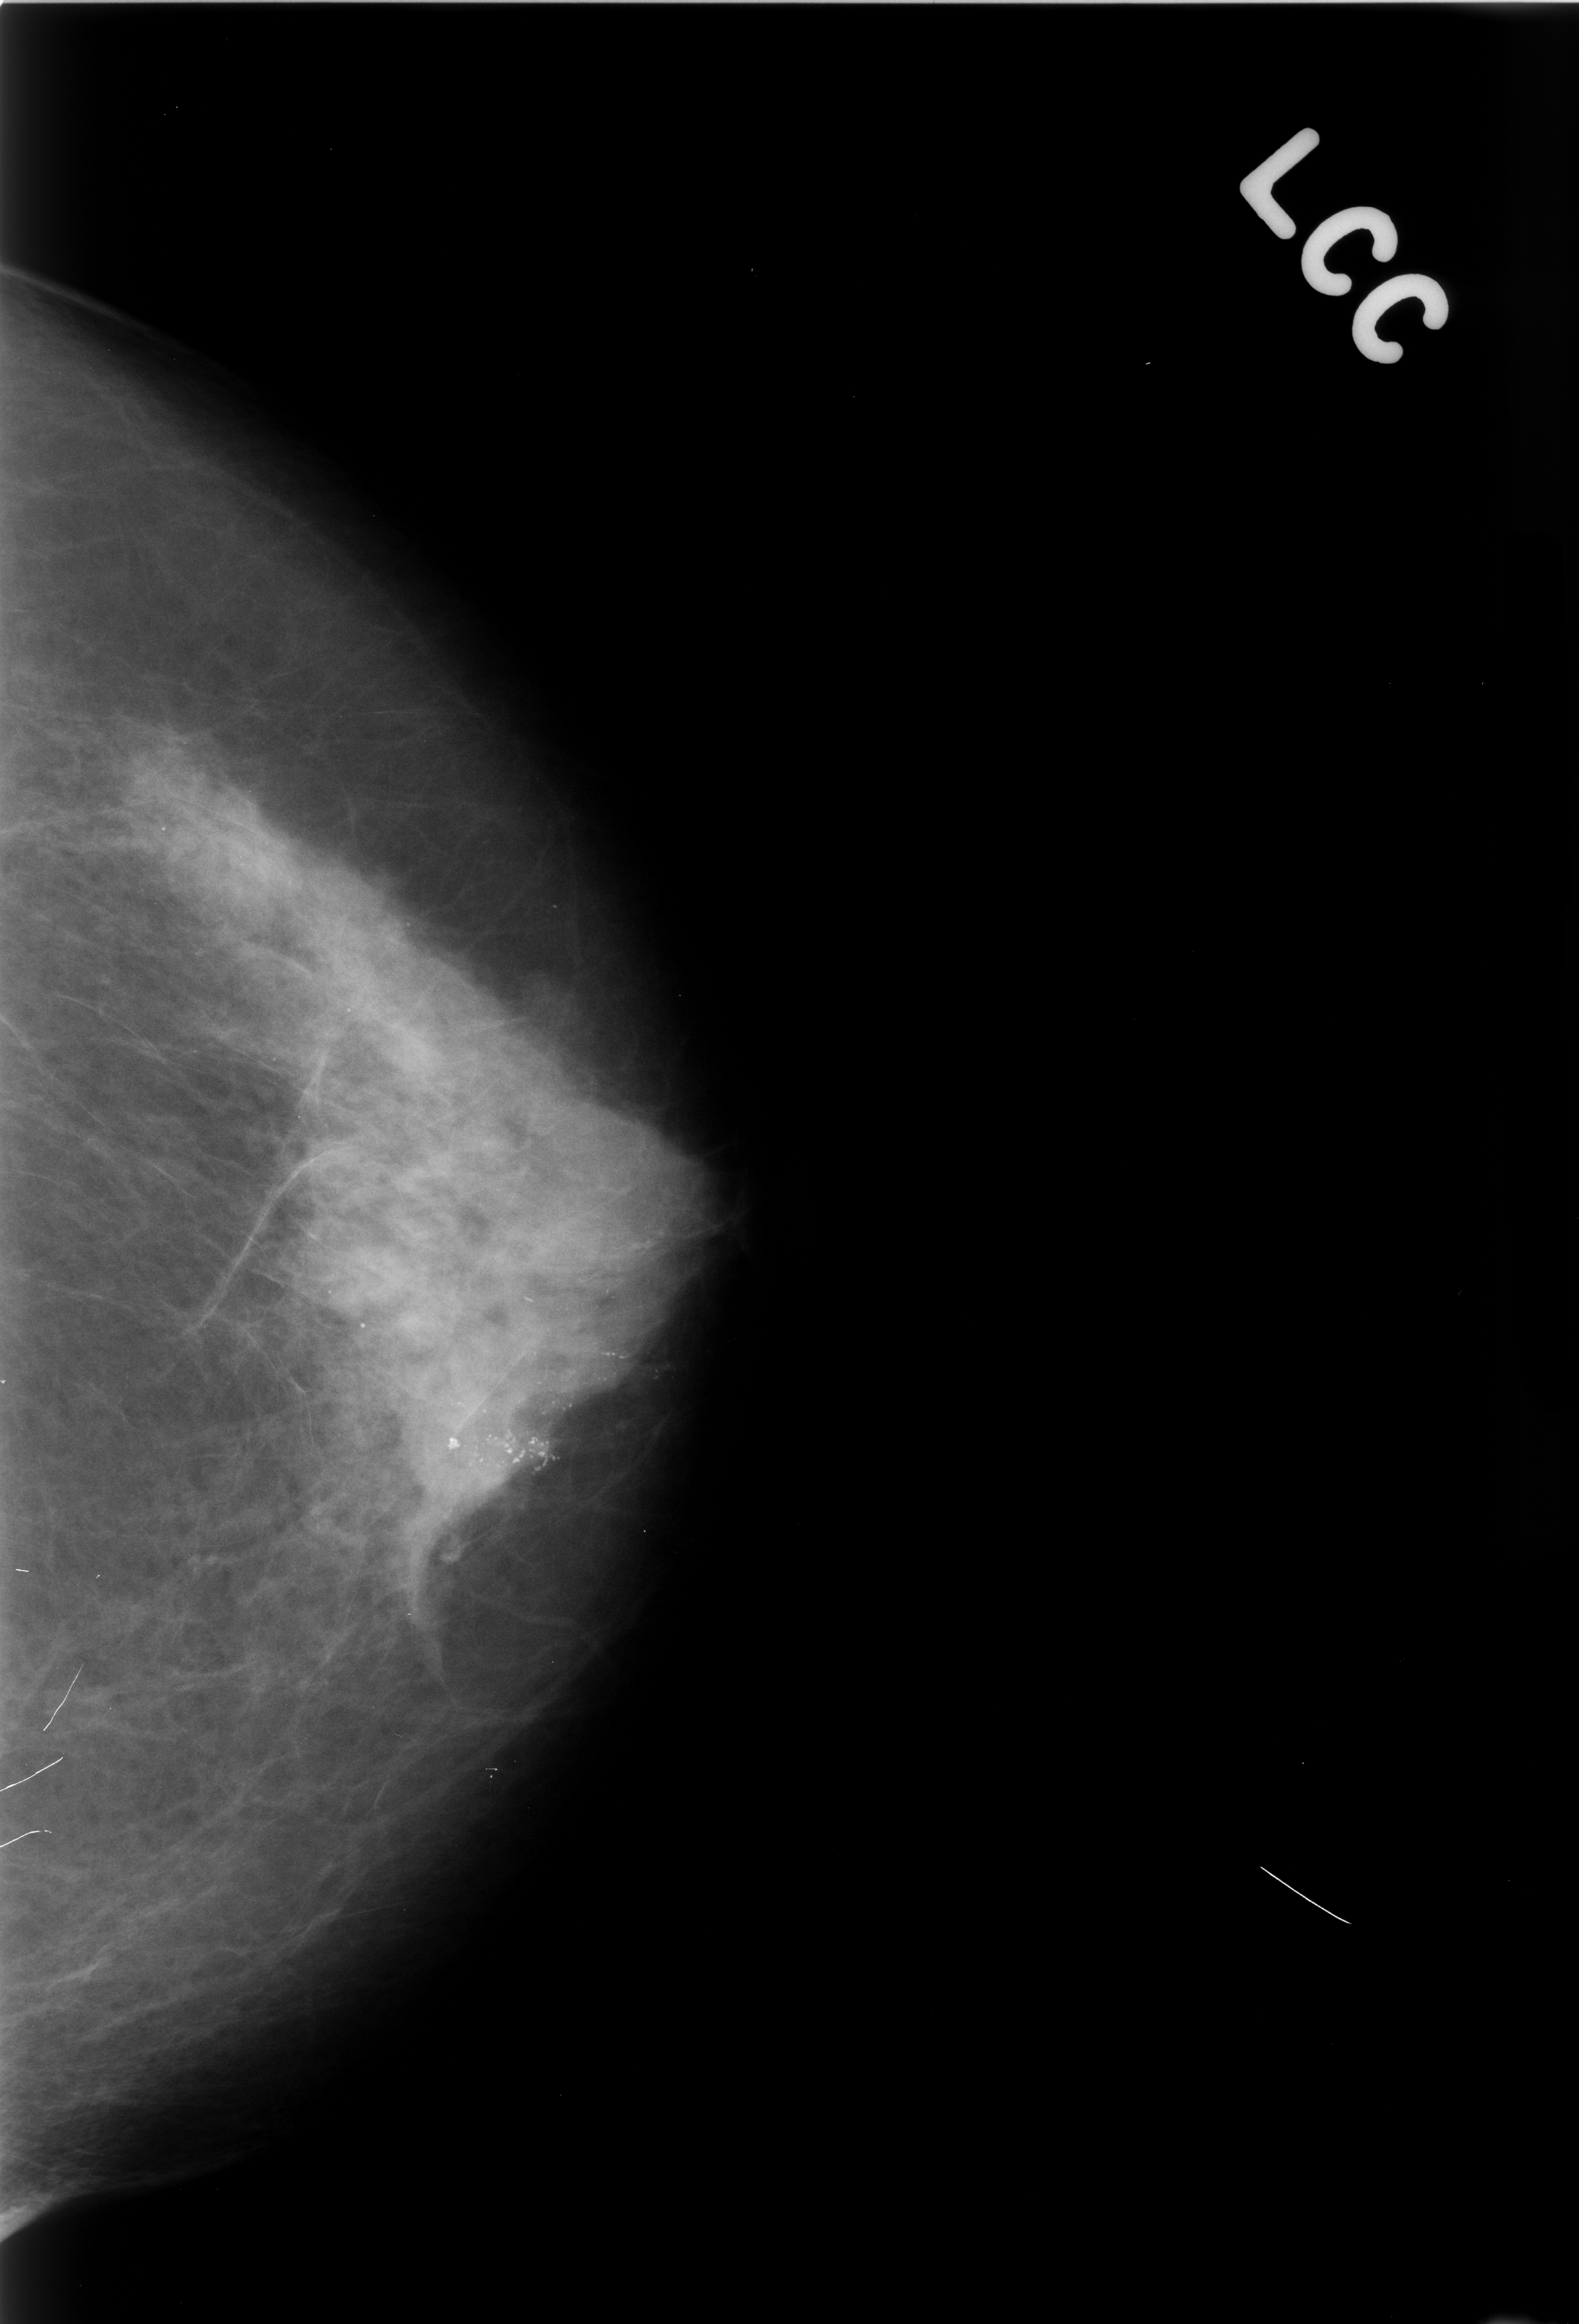
Digitized screen-film mammogram; left breast; CC view; breast composition: heterogeneously dense (BI-RADS density category 3 of 4); 1579 × 2324 image matrix.
Marked abnormalities (boxes around the expert regions of interest):
- calcifications, morphology pleomorphic, distribution segmental; BI-RADS assessment category 5; pathology result (as recorded, not read from the image): malignant: box from (x=229, y=1230) to (x=678, y=1776) px